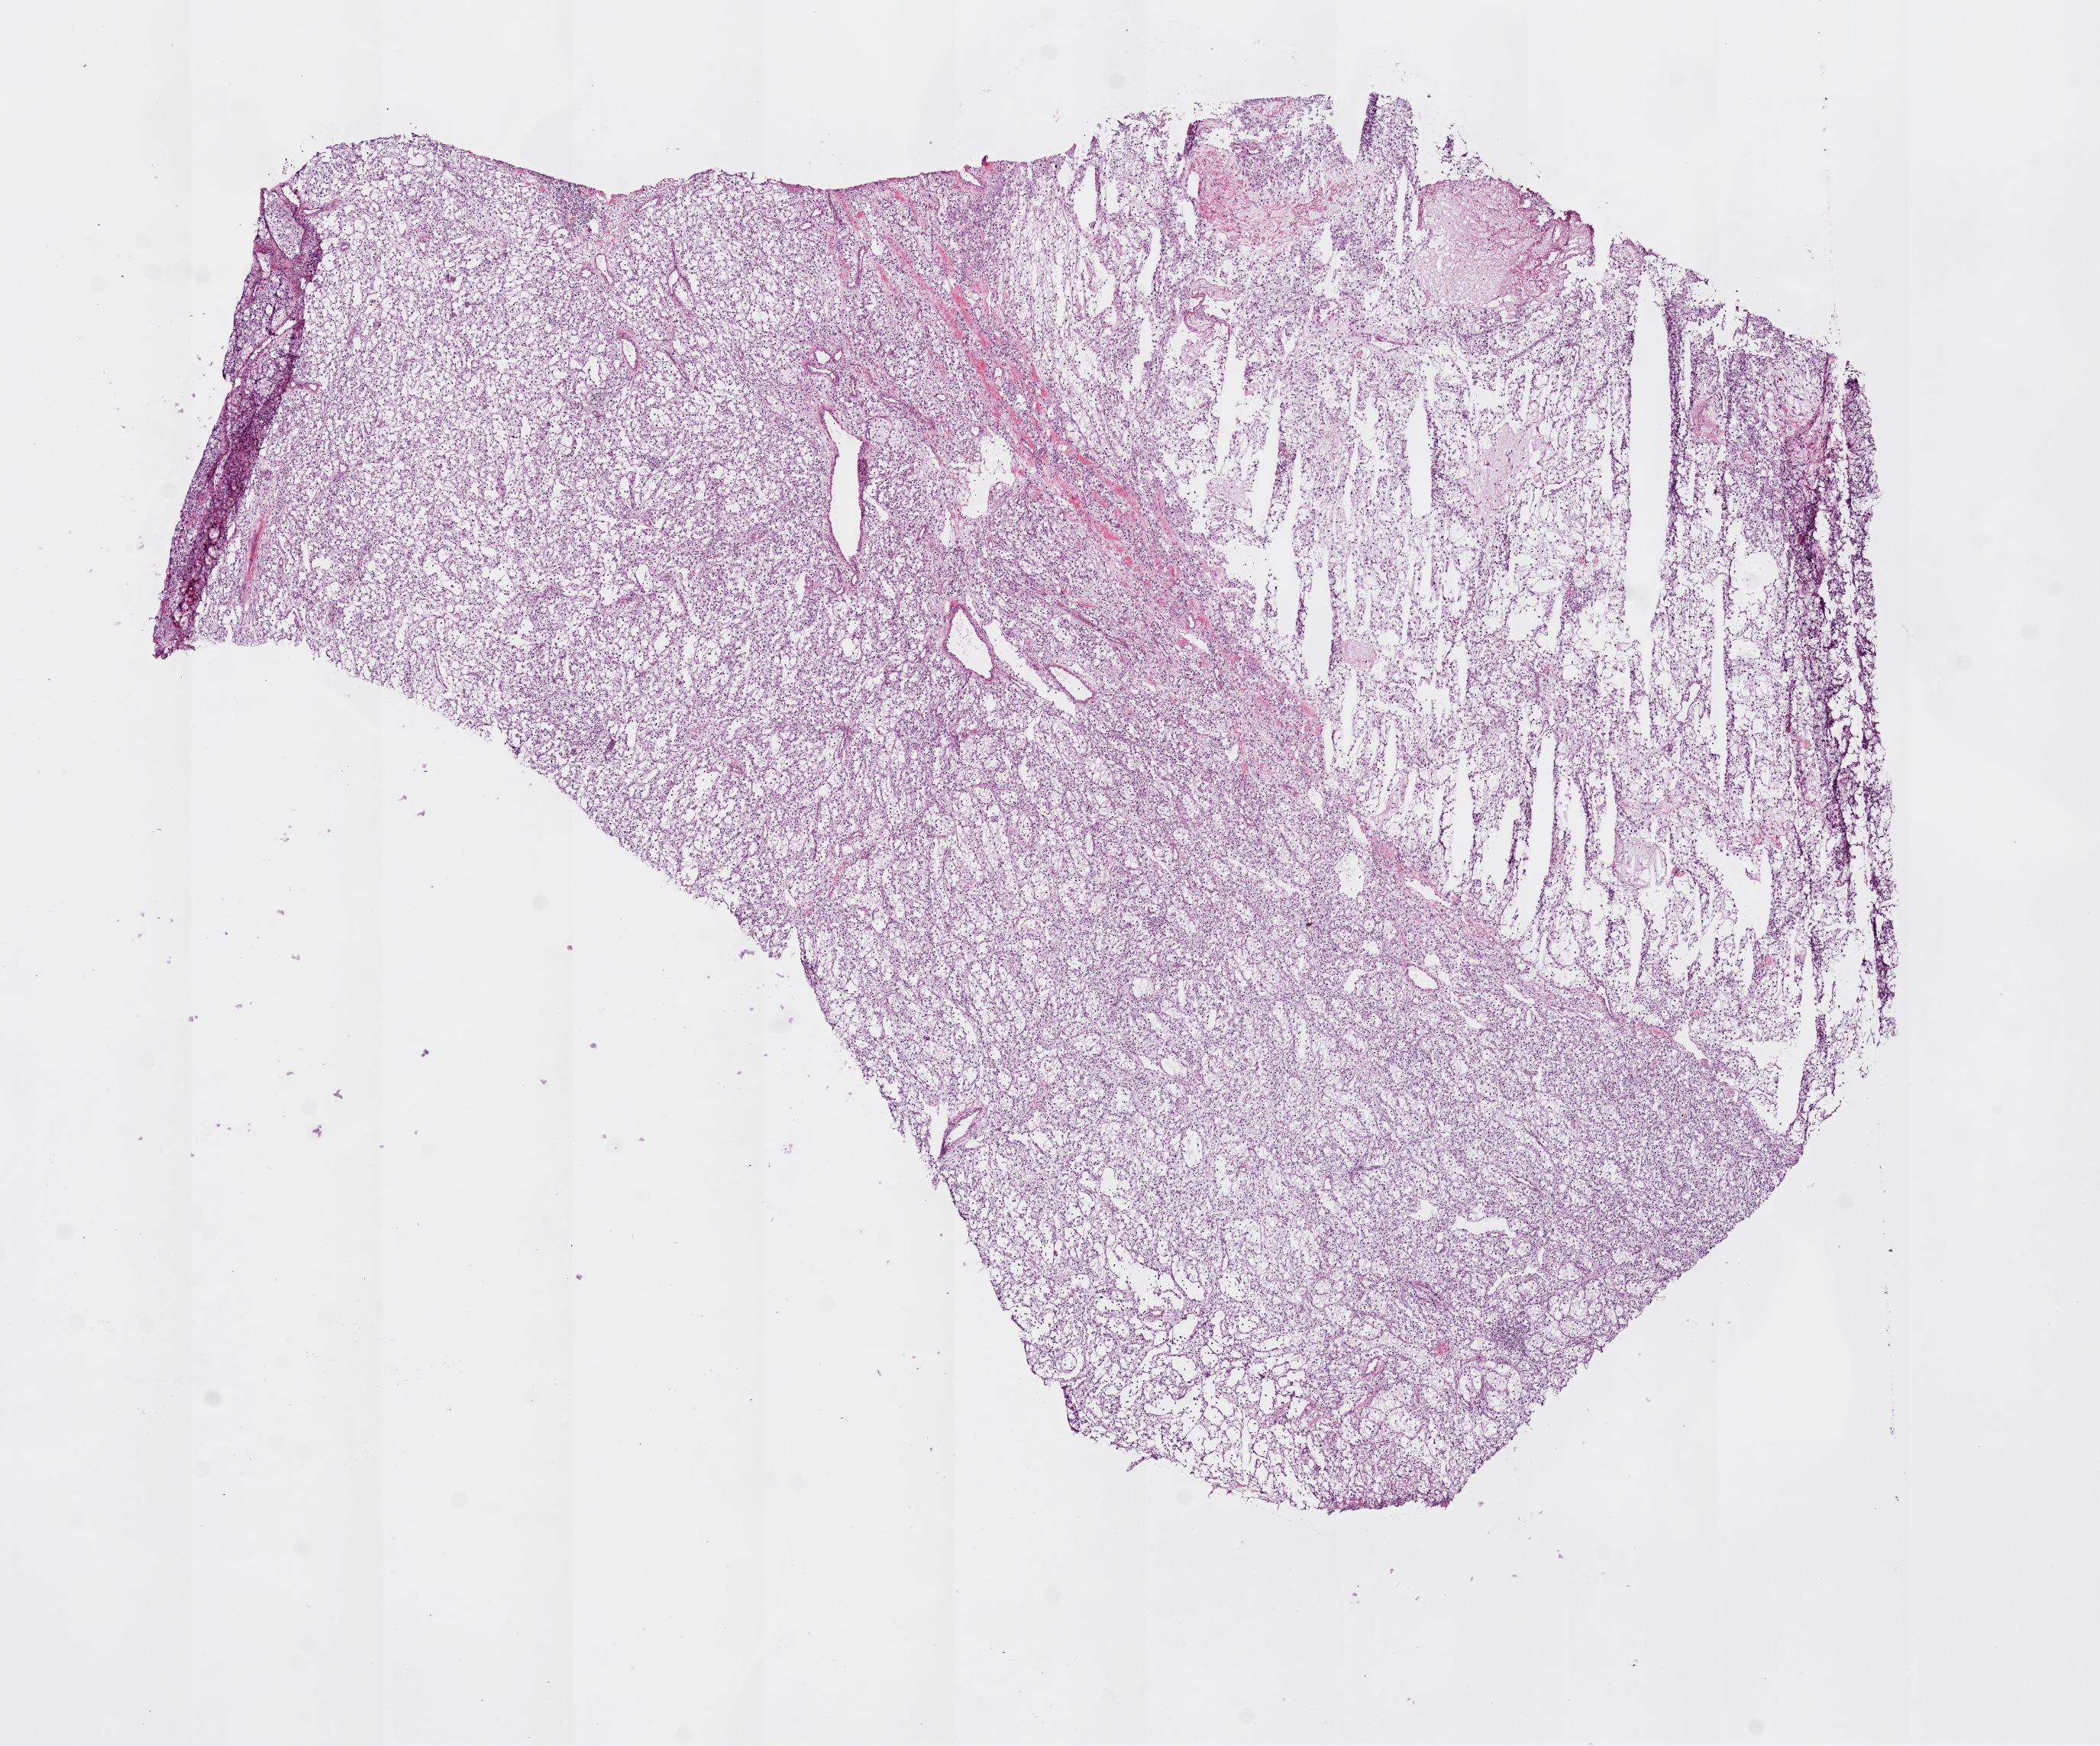
Digitized H&E-stained tissue section (whole slide) — low-resolution overview of the scanned area, about 11.0 x 9.2 mm (from a 20x scan), frozen section from the bottom of the tissue portion, primary tumour sample from the kidney. Female, age 78 years at initial diagnosis. Histologic grade: G2 (moderately differentiated). Composition of this section per pathologist review: tumour cells 90%, tumour nuclei 85%, normal cells 0%, stromal cells 10%, necrosis 0%.
• AJCC pathologic stage: I
• laterality: right
• pathologic diagnosis: Clear cell adenocarcinoma, NOS